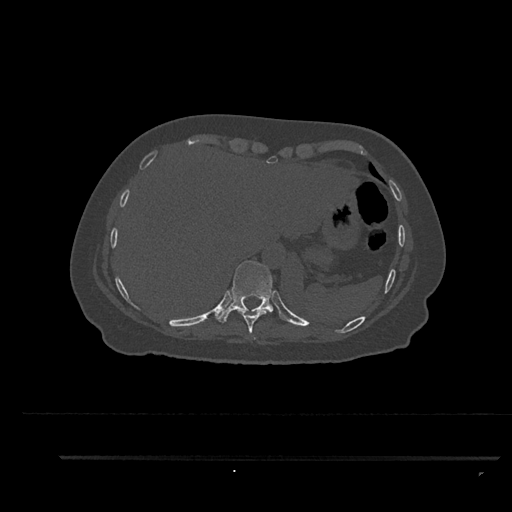
CT including the spine, one axial slice; slice 387 of 797 in the series (ordered by position); reconstruction kernel Br40s/3; bone window (W 1800 / L 400 HU); 0.5 mm slice thickness; 512 × 512 image matrix. Female patient, age 44 years. Case-level facts recorded for this patient, not image findings: primary cancer: renal.
Outlined on this slice (semi-automatically segmented with operator editing):
- T10 vertebra: bounding box [x1, y1, x2, y2] px = [215, 260, 281, 323]
- T9 vertebra: [237, 309, 267, 340]